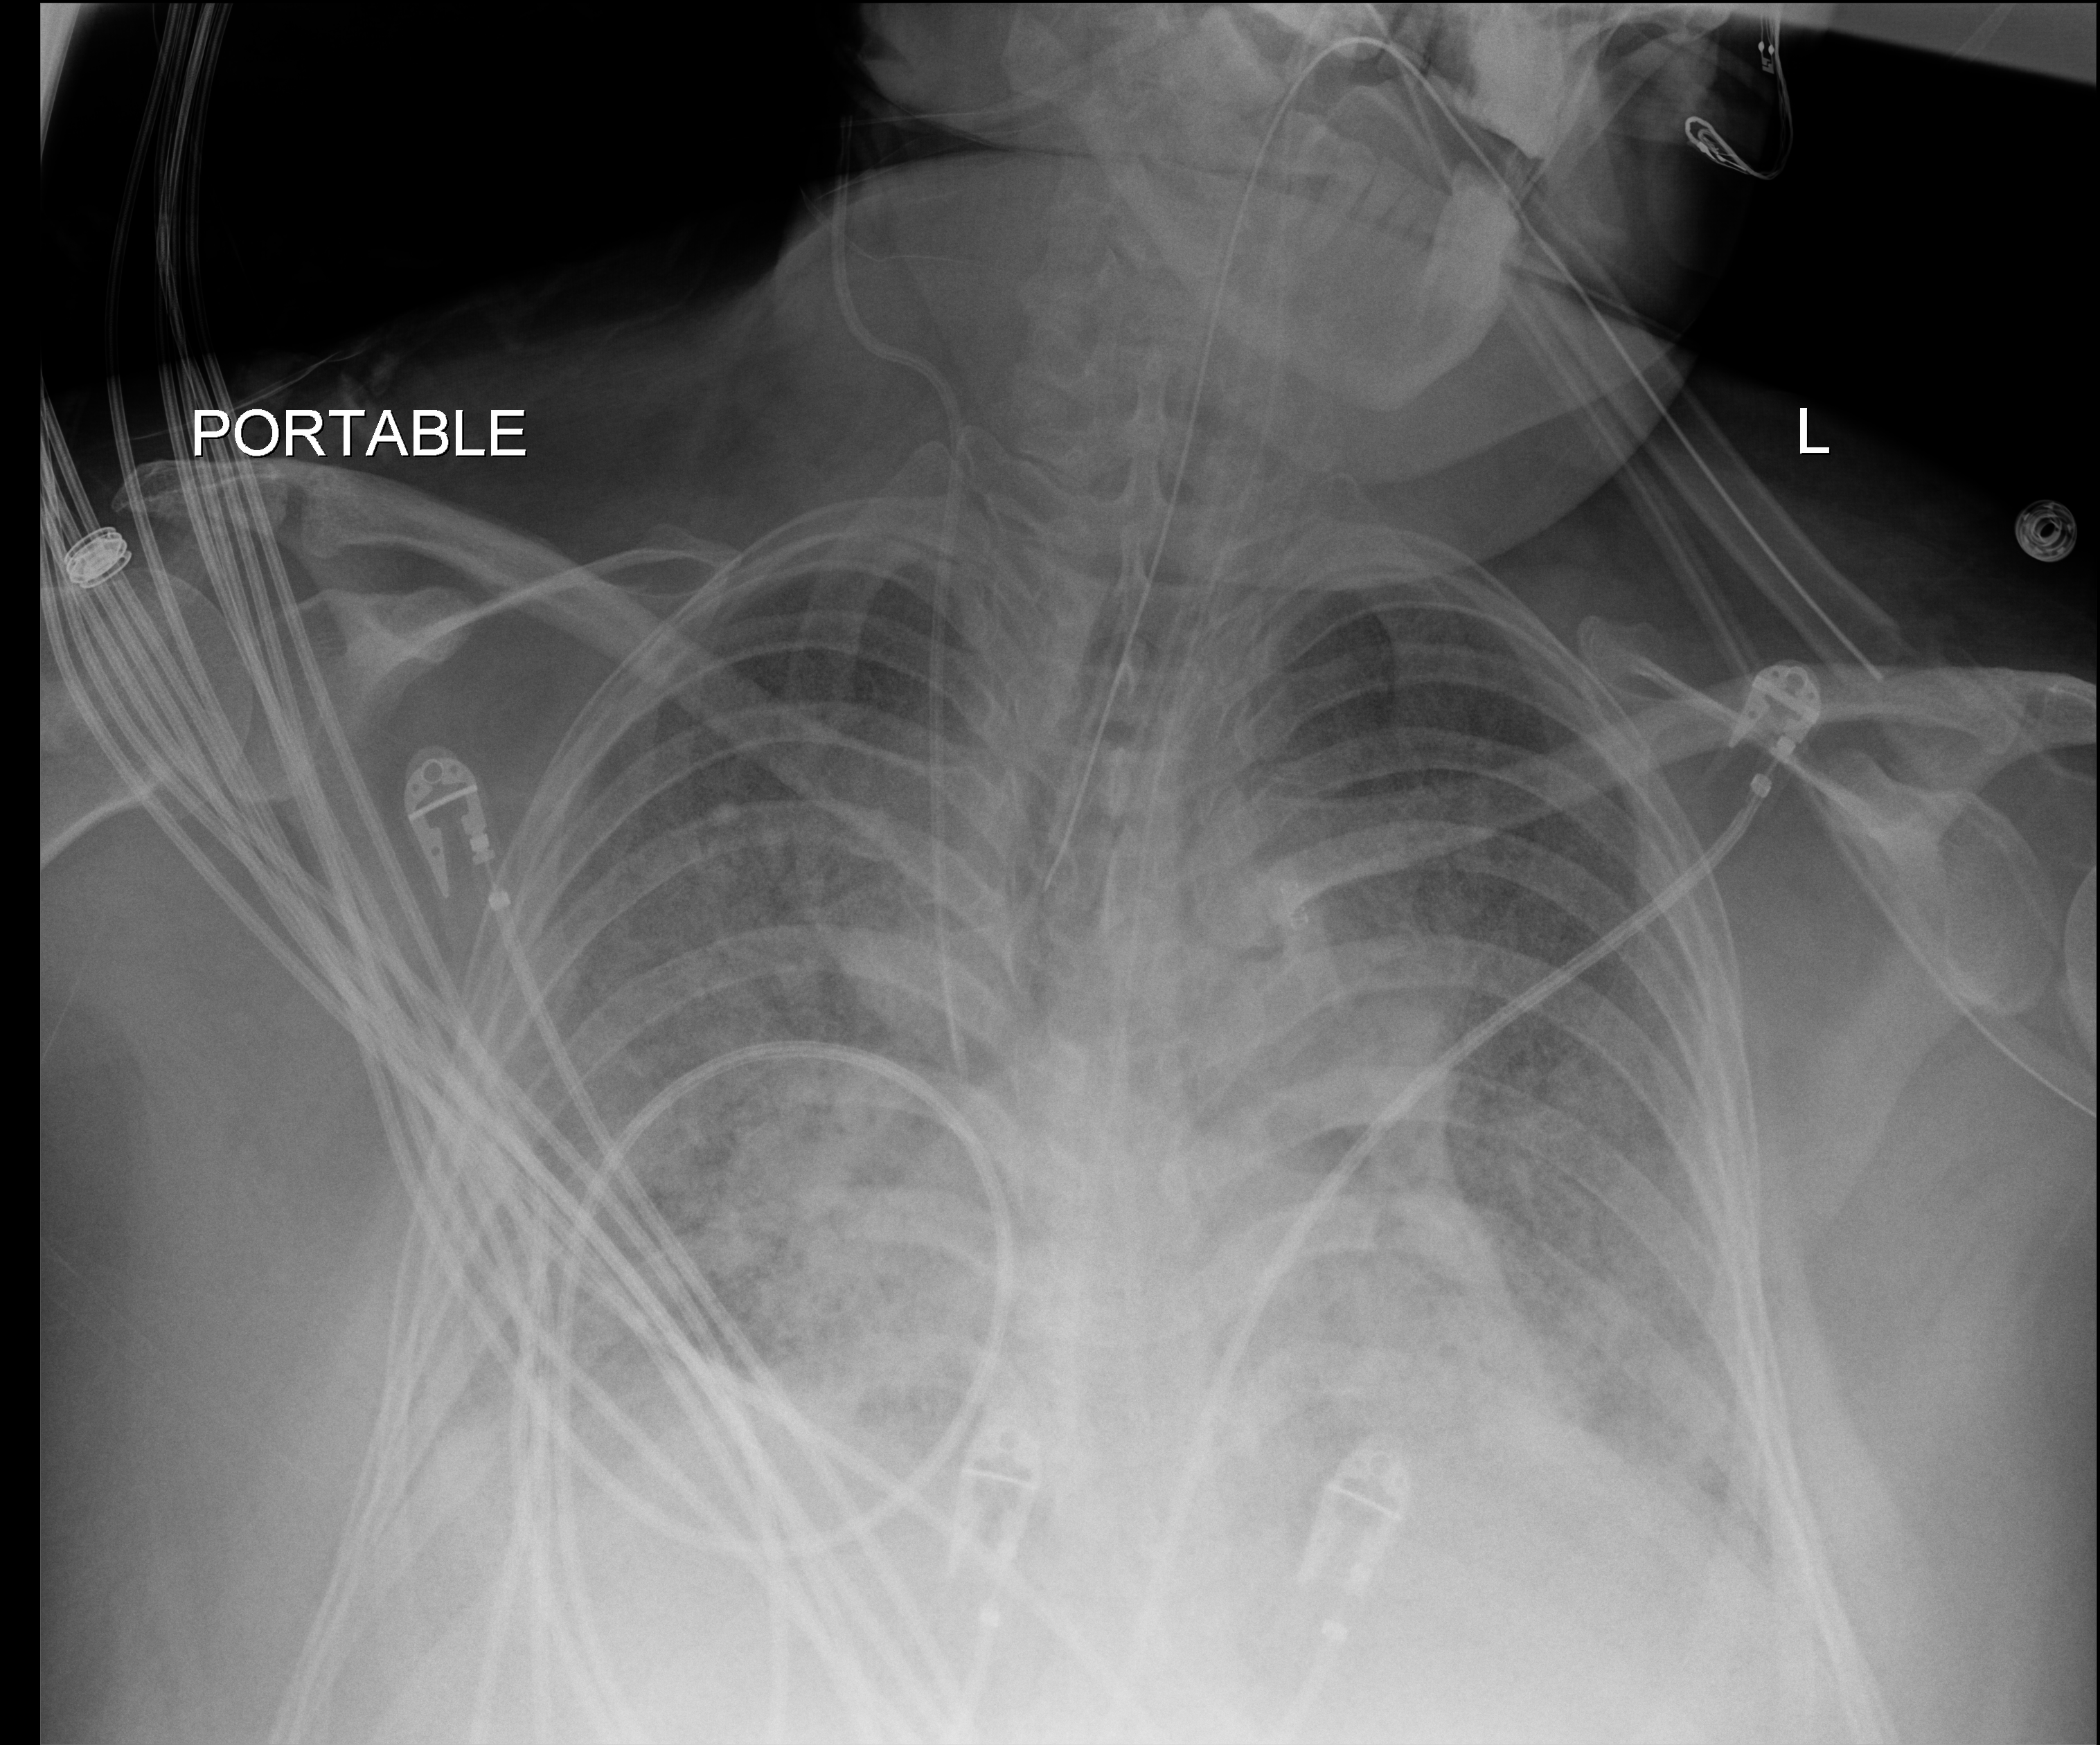
Portable chest radiograph, anteroposterior (AP) projection. Adult patient hospitalised with COVID-19, age 18–59 years.
Hospital-stay facts (about this admission, not read from this image; timing relative to this image not recorded):
- mechanically ventilated during this hospital stay: yes